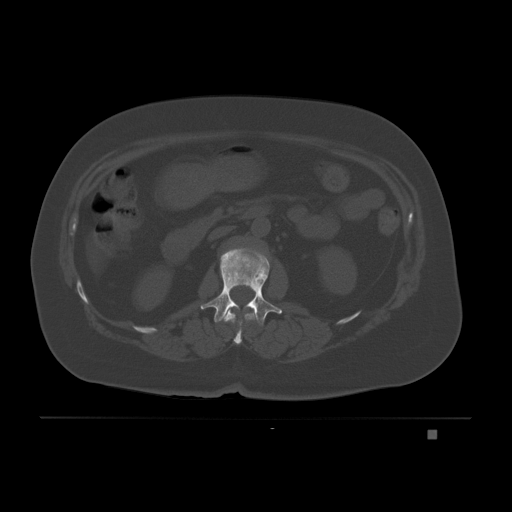
CT including the spine, one axial slice. Position 71 of 221 along the scan axis. Bone window (W 1800 / L 400 HU). 3 mm slice thickness. 512 × 512 image matrix, field of view 474 × 474 mm. Patient: female, 63 years. From the clinical record (not read from this slice): primary cancer: breast.
Structures marked on this image (semi-automatically segmented with operator editing):
- L1 vertebra: box from (x=200, y=247) to (x=282, y=325) px
- T12 vertebra: (x=224, y=310)–(x=256, y=345)